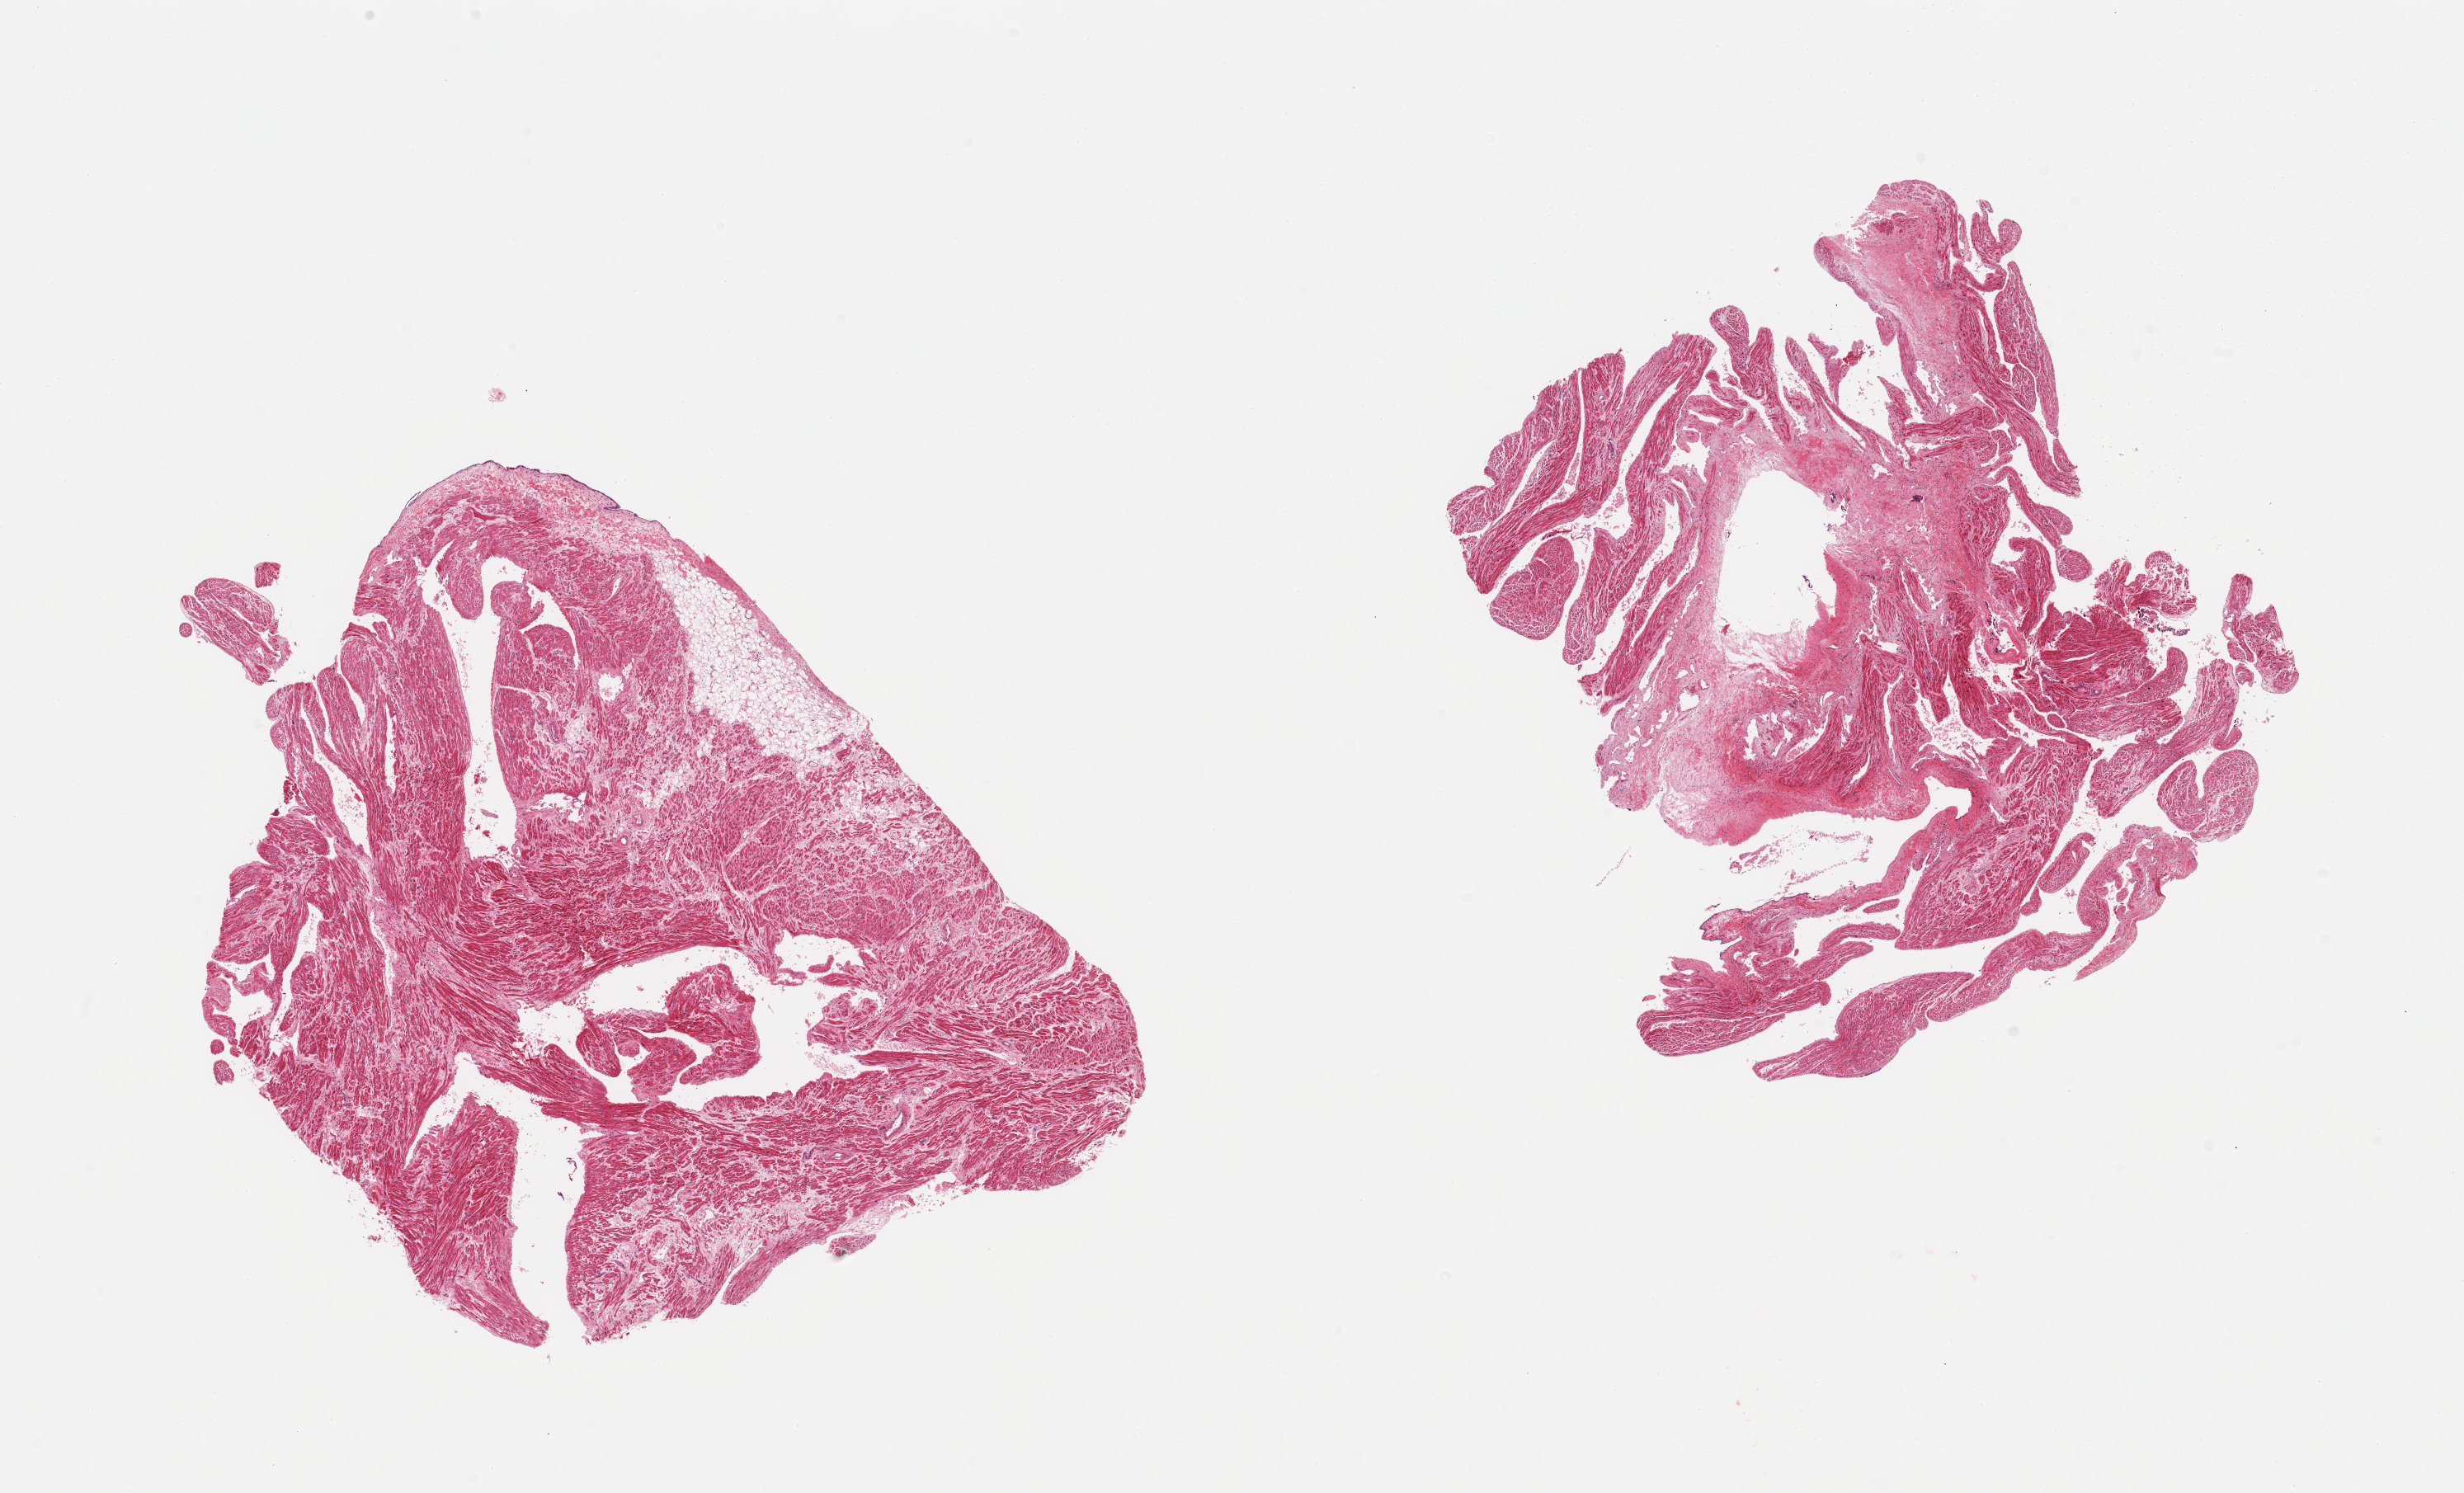
Hematoxylin and eosin (H&E) whole-slide image, whole scanned area (about 23.6 x 14.3 mm) shown as a low-resolution overview. PAXgene-fixed, paraffin-embedded tissue. Section of auricular appendage (target tissue). Donor tissue sample.
Pathologist's review note for this sample: 2 pieces; 10% adipose in 1; 30% fibrous content in other.